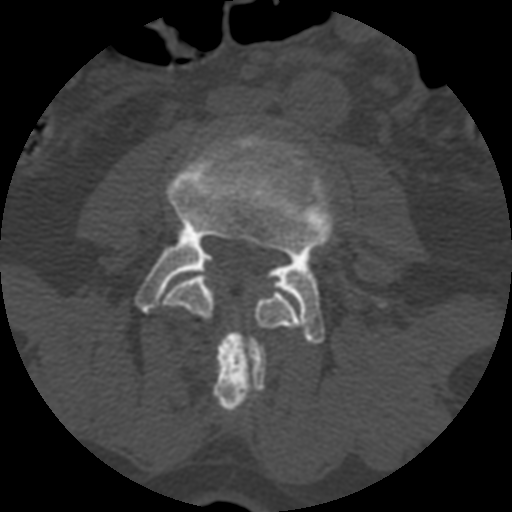
CT including the spine, one axial slice; position 291 of 399 along the scan axis; reconstruction kernel STANDARD; 120 kVp; bone window (W 1800 / L 400 HU); 1.25 mm slice thickness; 512 × 512 image matrix. Patient age 71 years. Case-level facts recorded for this patient, not image findings: primary cancer: prostate.
Annotated regions visible in this slice (semi-automatically segmented with operator editing):
- L3 vertebra: box from (x=163, y=272) to (x=303, y=413) px
- L4 vertebra: (x=135, y=132)–(x=385, y=344)